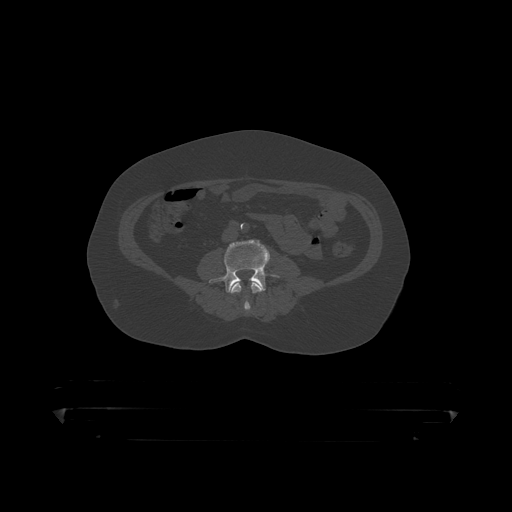
CT including the spine, one axial slice. Slice 73 of 390 in the series (ordered by position). Reconstruction kernel STANDARD. Bone window (W 1800 / L 400 HU). 1.25 mm slice thickness. 512 × 512 image matrix, field of view 650 × 650 mm. Male patient, age 60 years. Case-level facts recorded for this patient, not image findings: primary cancer: prostate.
Structures marked on this image (semi-automatic segmentation, software-assisted and operator-edited):
- L3 vertebra: bounding box [x1, y1, x2, y2] px = [230, 282, 264, 314]
- L4 vertebra: [209, 239, 271, 293]